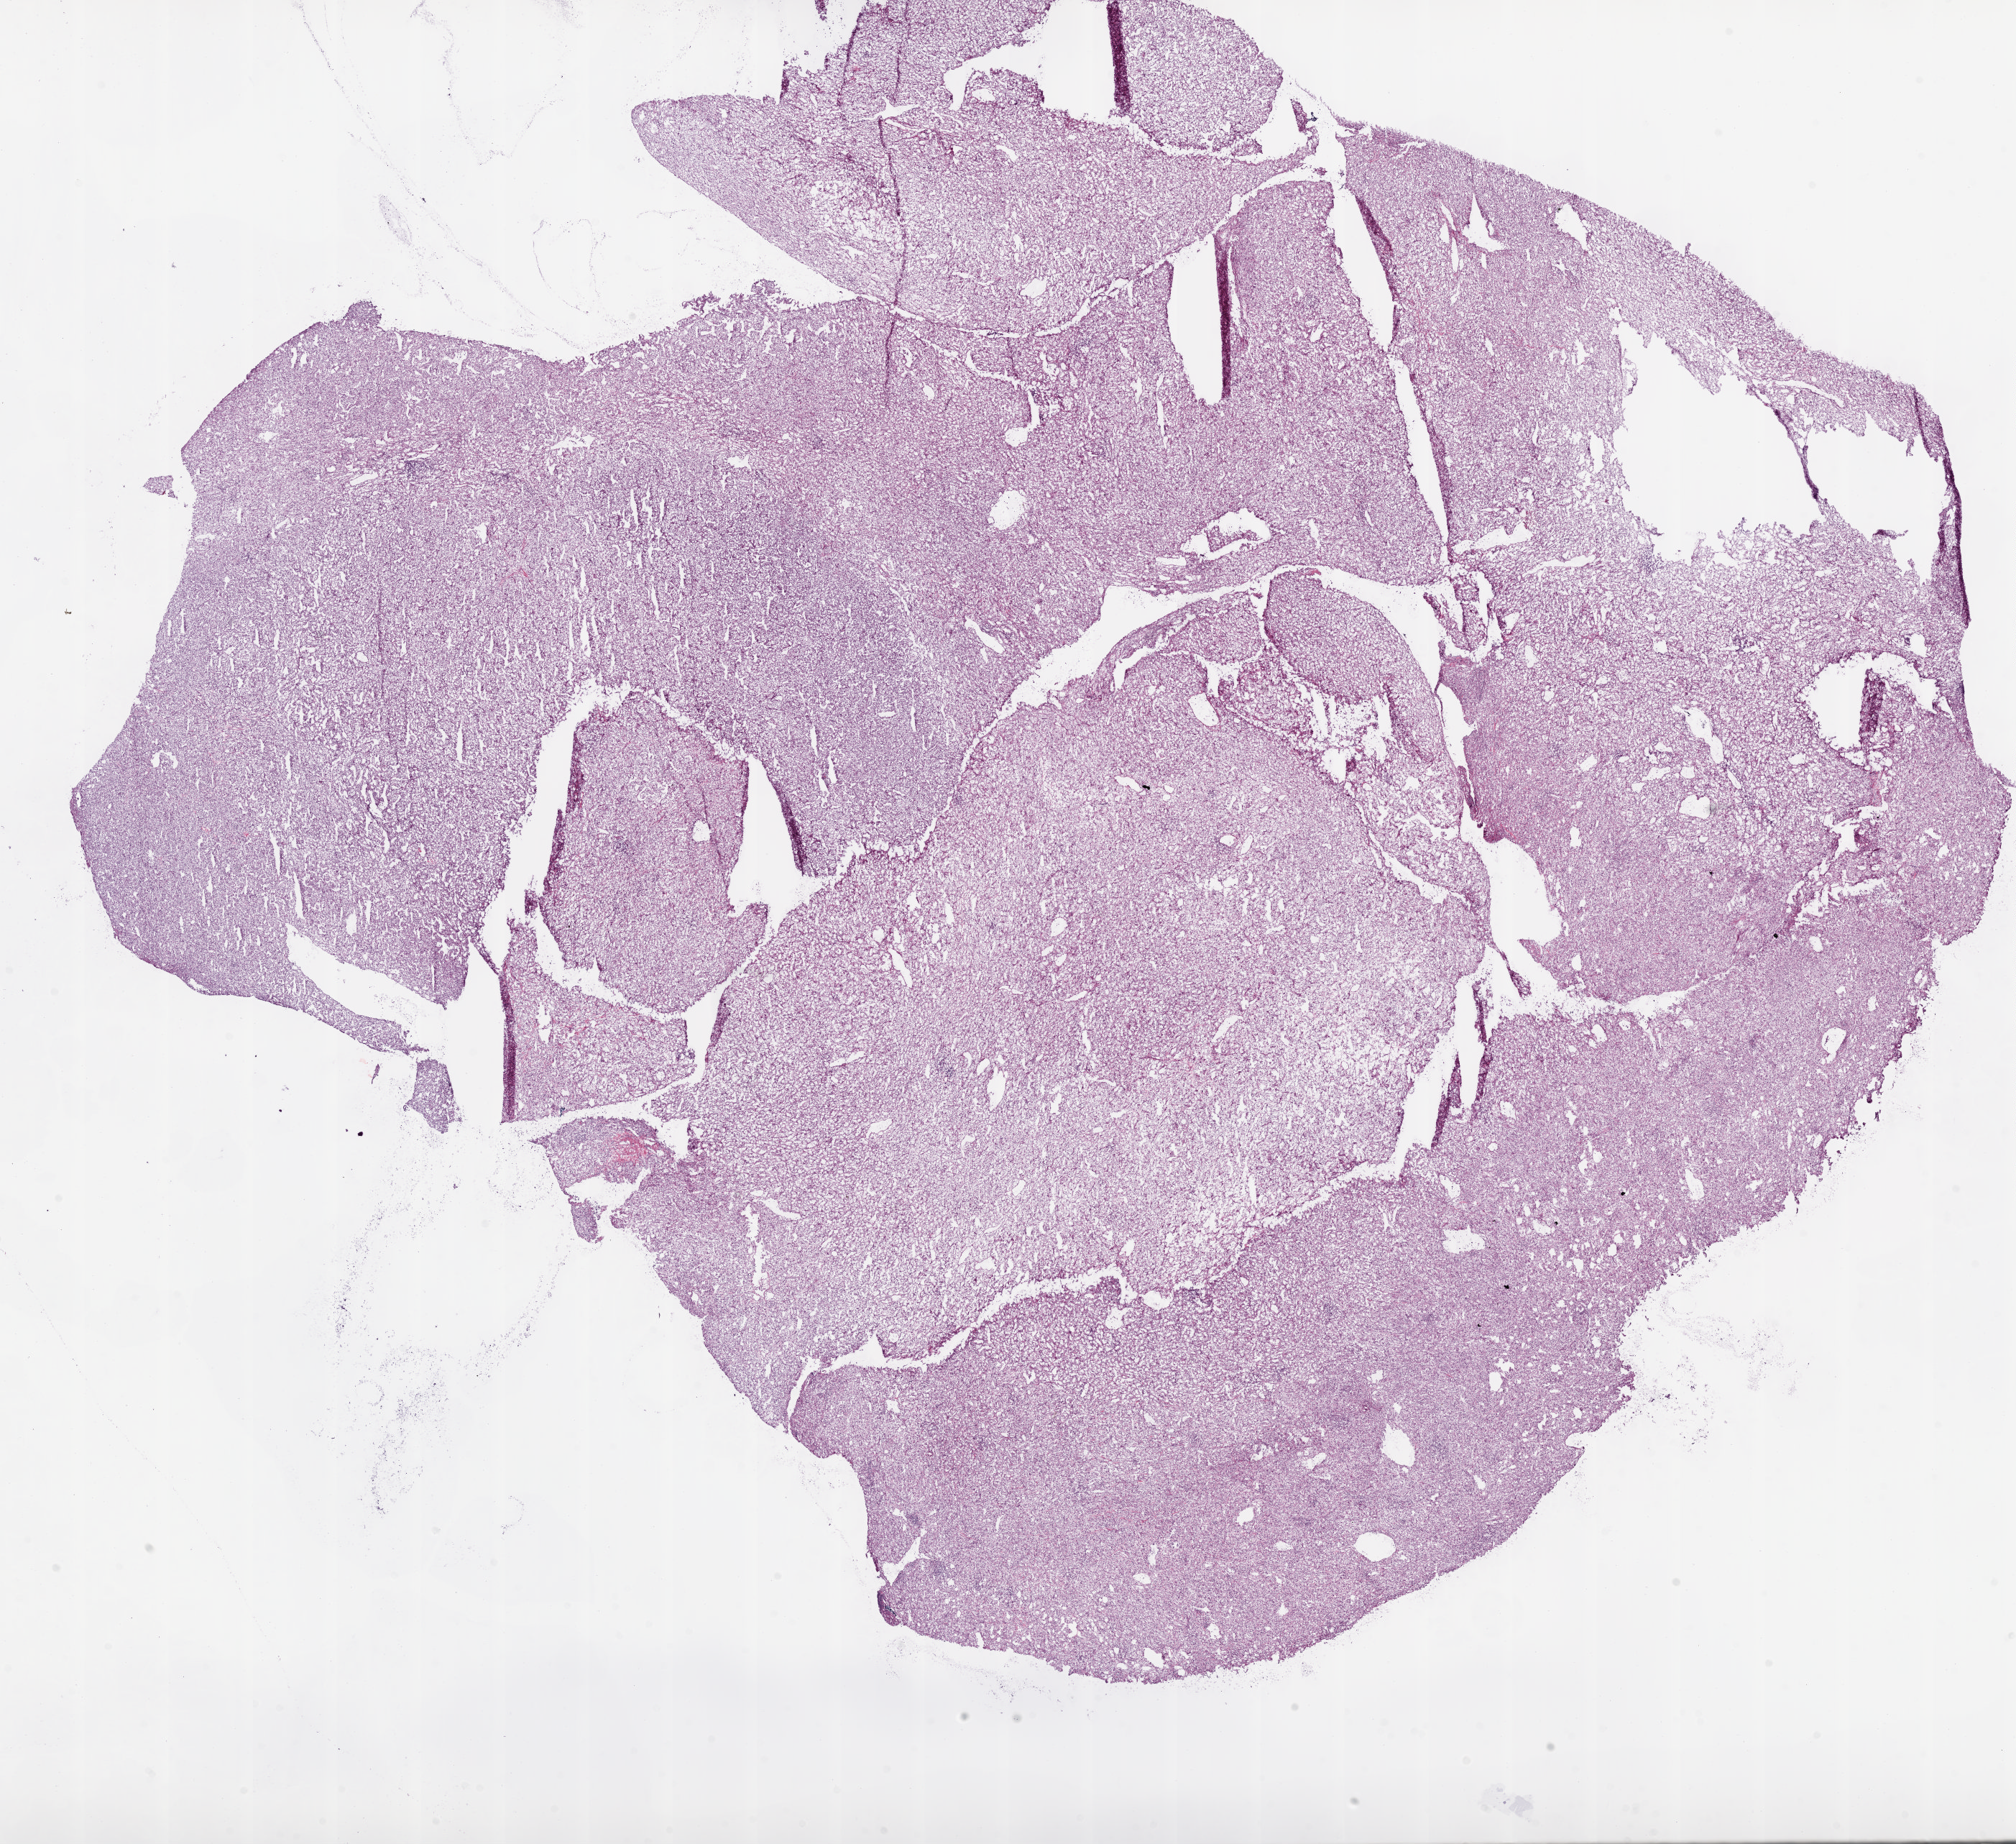
Digitized Hematoxylin and eosin (H&E) stained tissue section (whole slide), a low-resolution overview of the entire scanned area, about 22.5 x 20.6 mm (from a 5x scan), frozen section from the top of the tissue portion, sample: primary tumour, kidney. Male, age 46 years at initial diagnosis.
Pathologic diagnosis: Clear cell adenocarcinoma, NOS.